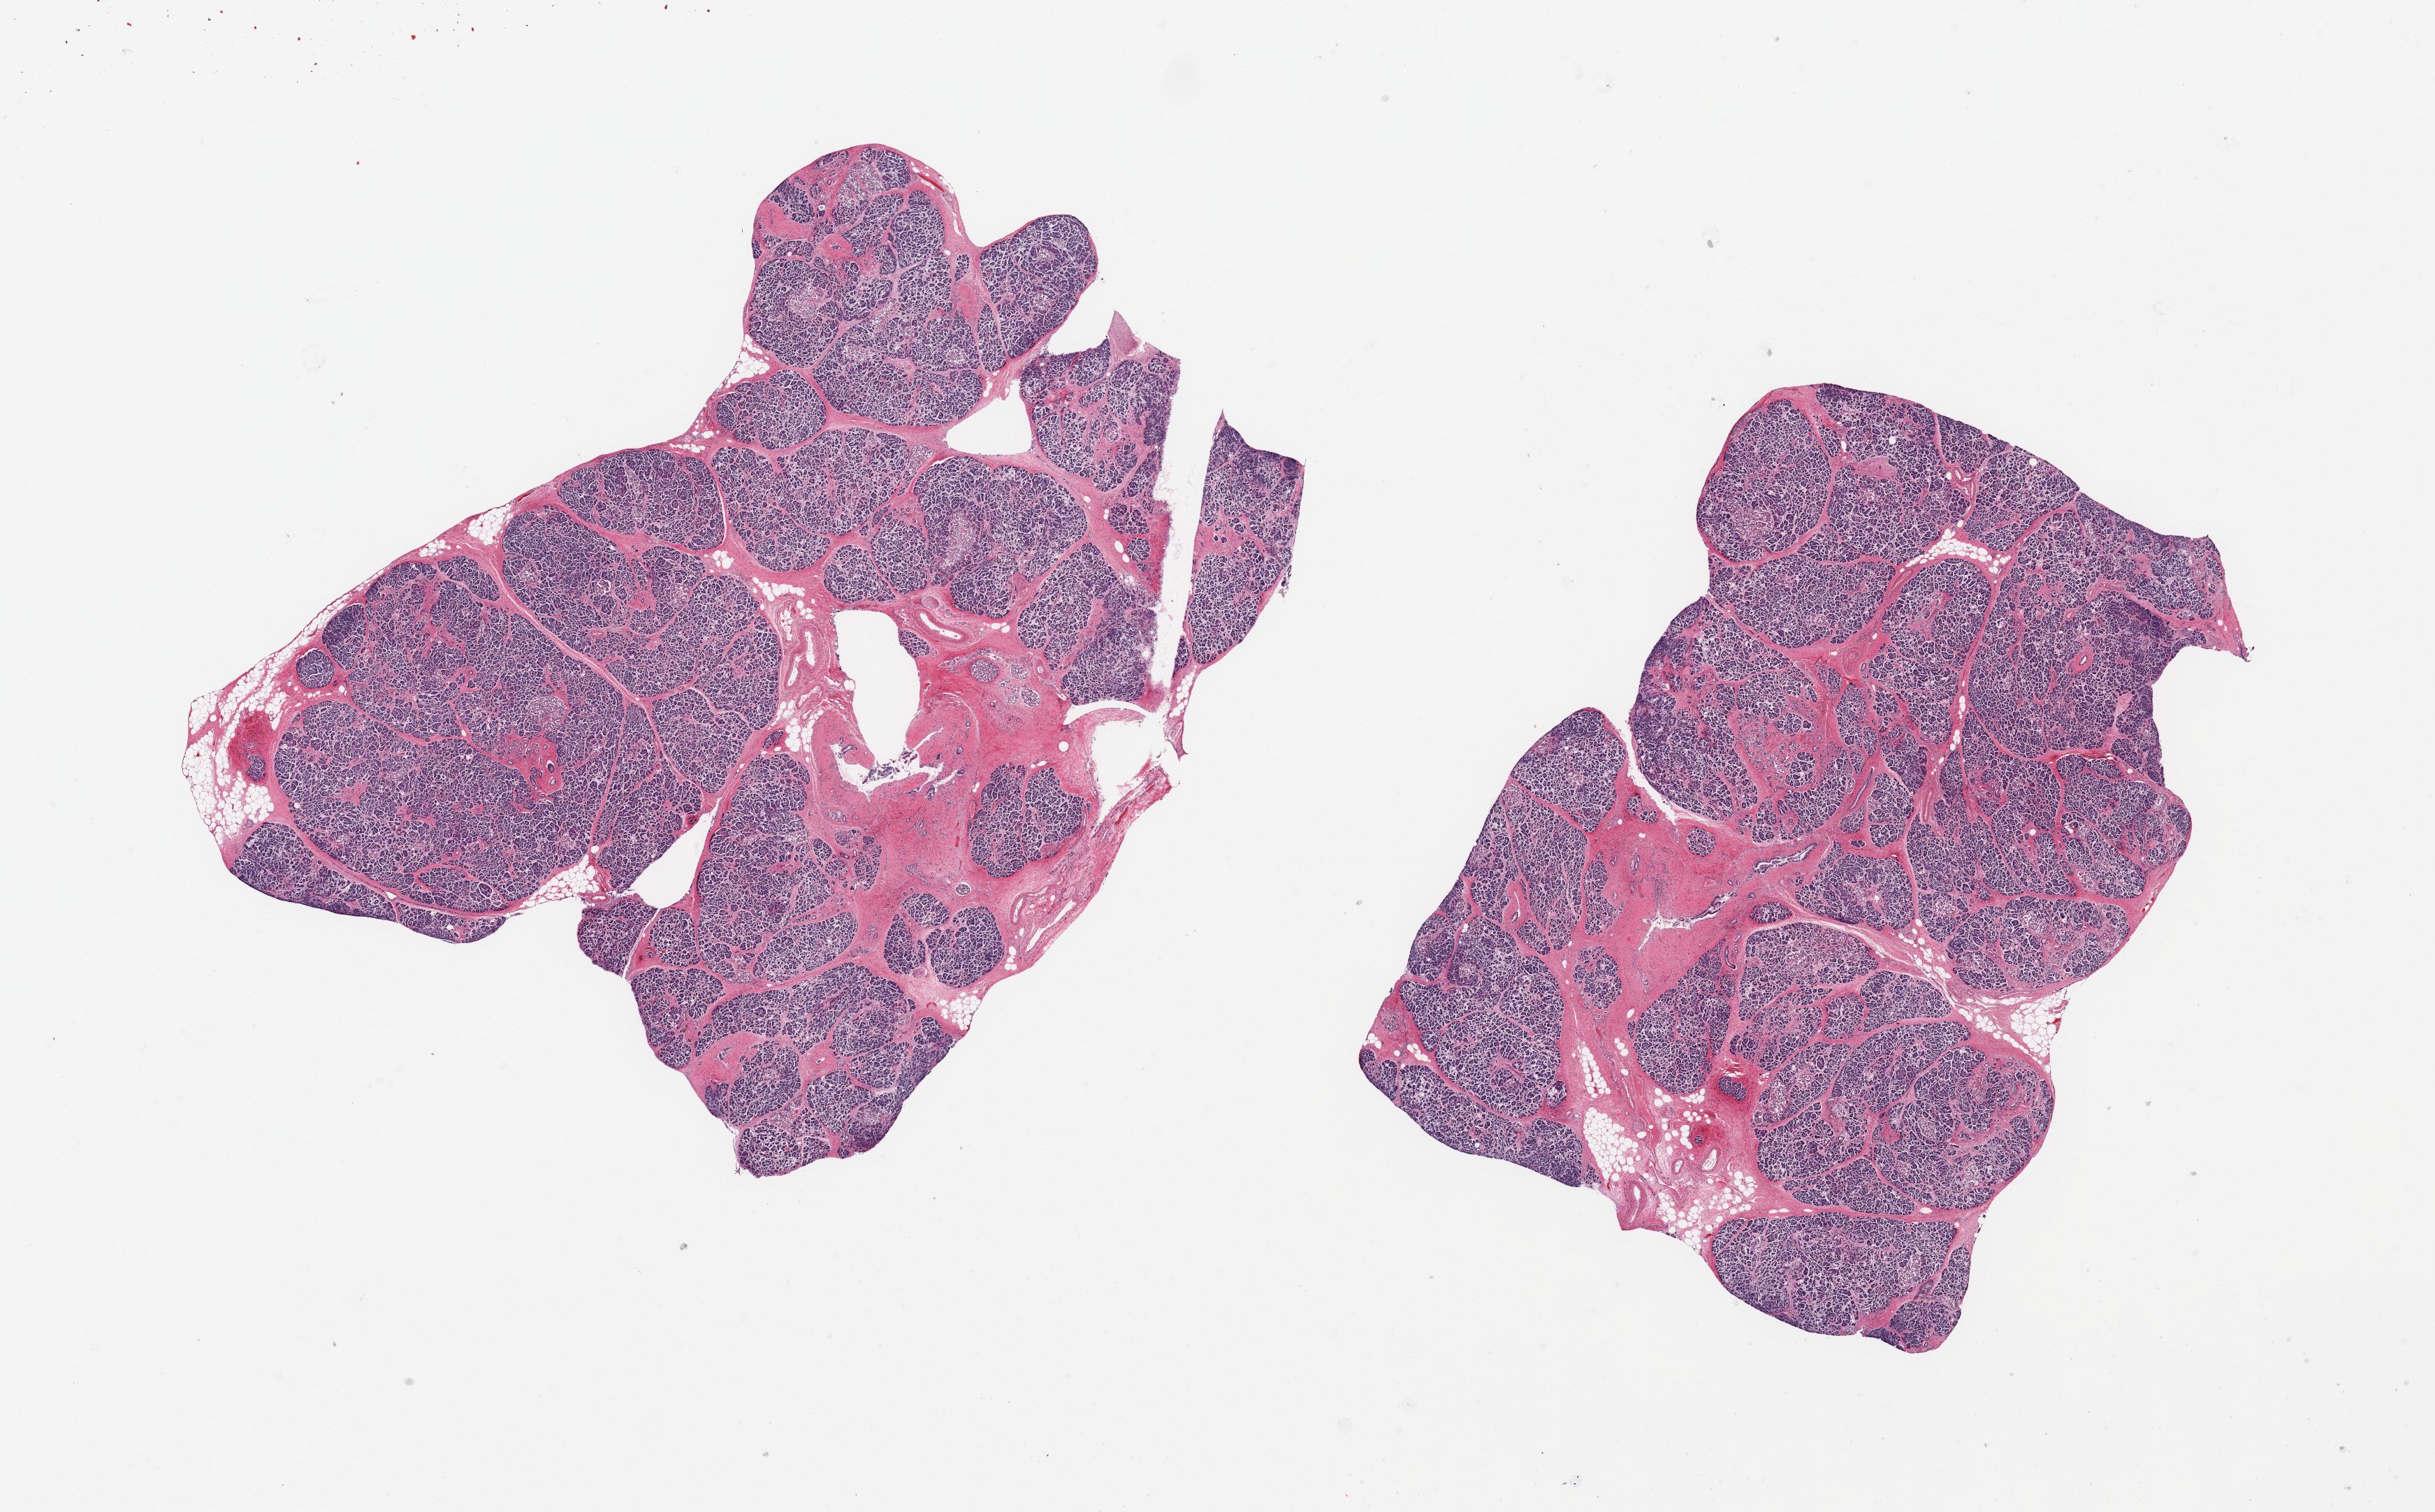
Hematoxylin and eosin (H&E) whole-slide image — a low-resolution overview of the entire scanned area, about 27.6 x 17.1 mm, PAXgene-fixed, paraffin-embedded tissue, sampled site (target tissue): pancreas, tissue donor sample. Donor: male.
Review note (as recorded): 2 pieces; moderate interstitial fibrosis with parenchymal atrophy.